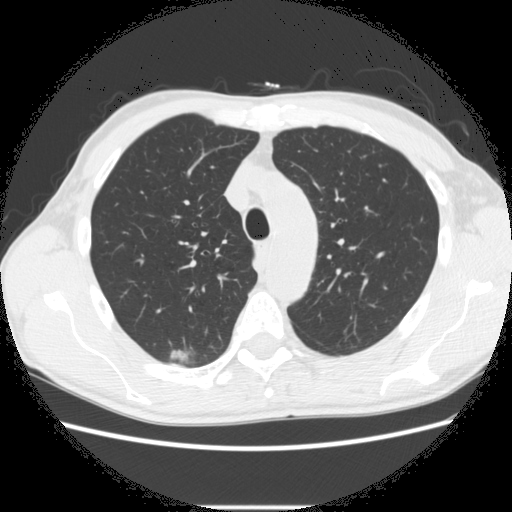
Axial slice from a low-dose chest CT screening exam. Second screening round (one year after baseline). Lung window (W 1500 / L -600 HU). 2.5 mm slice thickness. 512 × 512 image matrix, field of view 360 × 360 mm. Male, age 66 years at enrolment.
Expert-annotated lung lesion, bounding box [x1, y1, x2, y2] px = [160, 336, 222, 371]. The screening reader recorded 5 non-calcified nodules or masses ≥4 mm on this exam (right lower lobe, right upper lobe, right upper lobe, right upper lobe, left lower lobe); which of them this box marks is not recorded. Participant outcome: lung cancer diagnosed 75 days after this screen — adenocarcinoma, NOS, right upper lobe, undifferentiated (G4), stage IA (AJCC 6th edition), 20 mm at pathology.